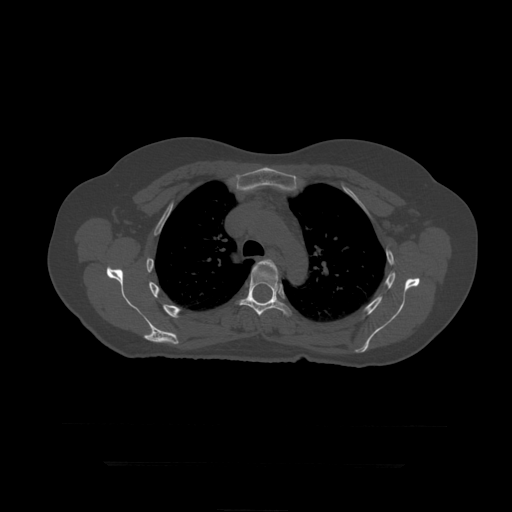
CT including the spine, one axial slice; position 322 of 399 along the scan axis; 120 kVp; bone window (W 1800 / L 400 HU); 1.25 mm slice thickness; 512 × 512 image matrix, field of view 450 × 450 mm. Patient age 41 years. Case-level facts recorded for this patient, not image findings: primary cancer: breast.
Structures marked on this image (semi-automatically segmented with operator editing):
- T5 vertebra: bounding box (x1, y1, x2, y2) in pixels: (256, 260, 279, 280)
- T6 vertebra: (239, 265, 292, 317)